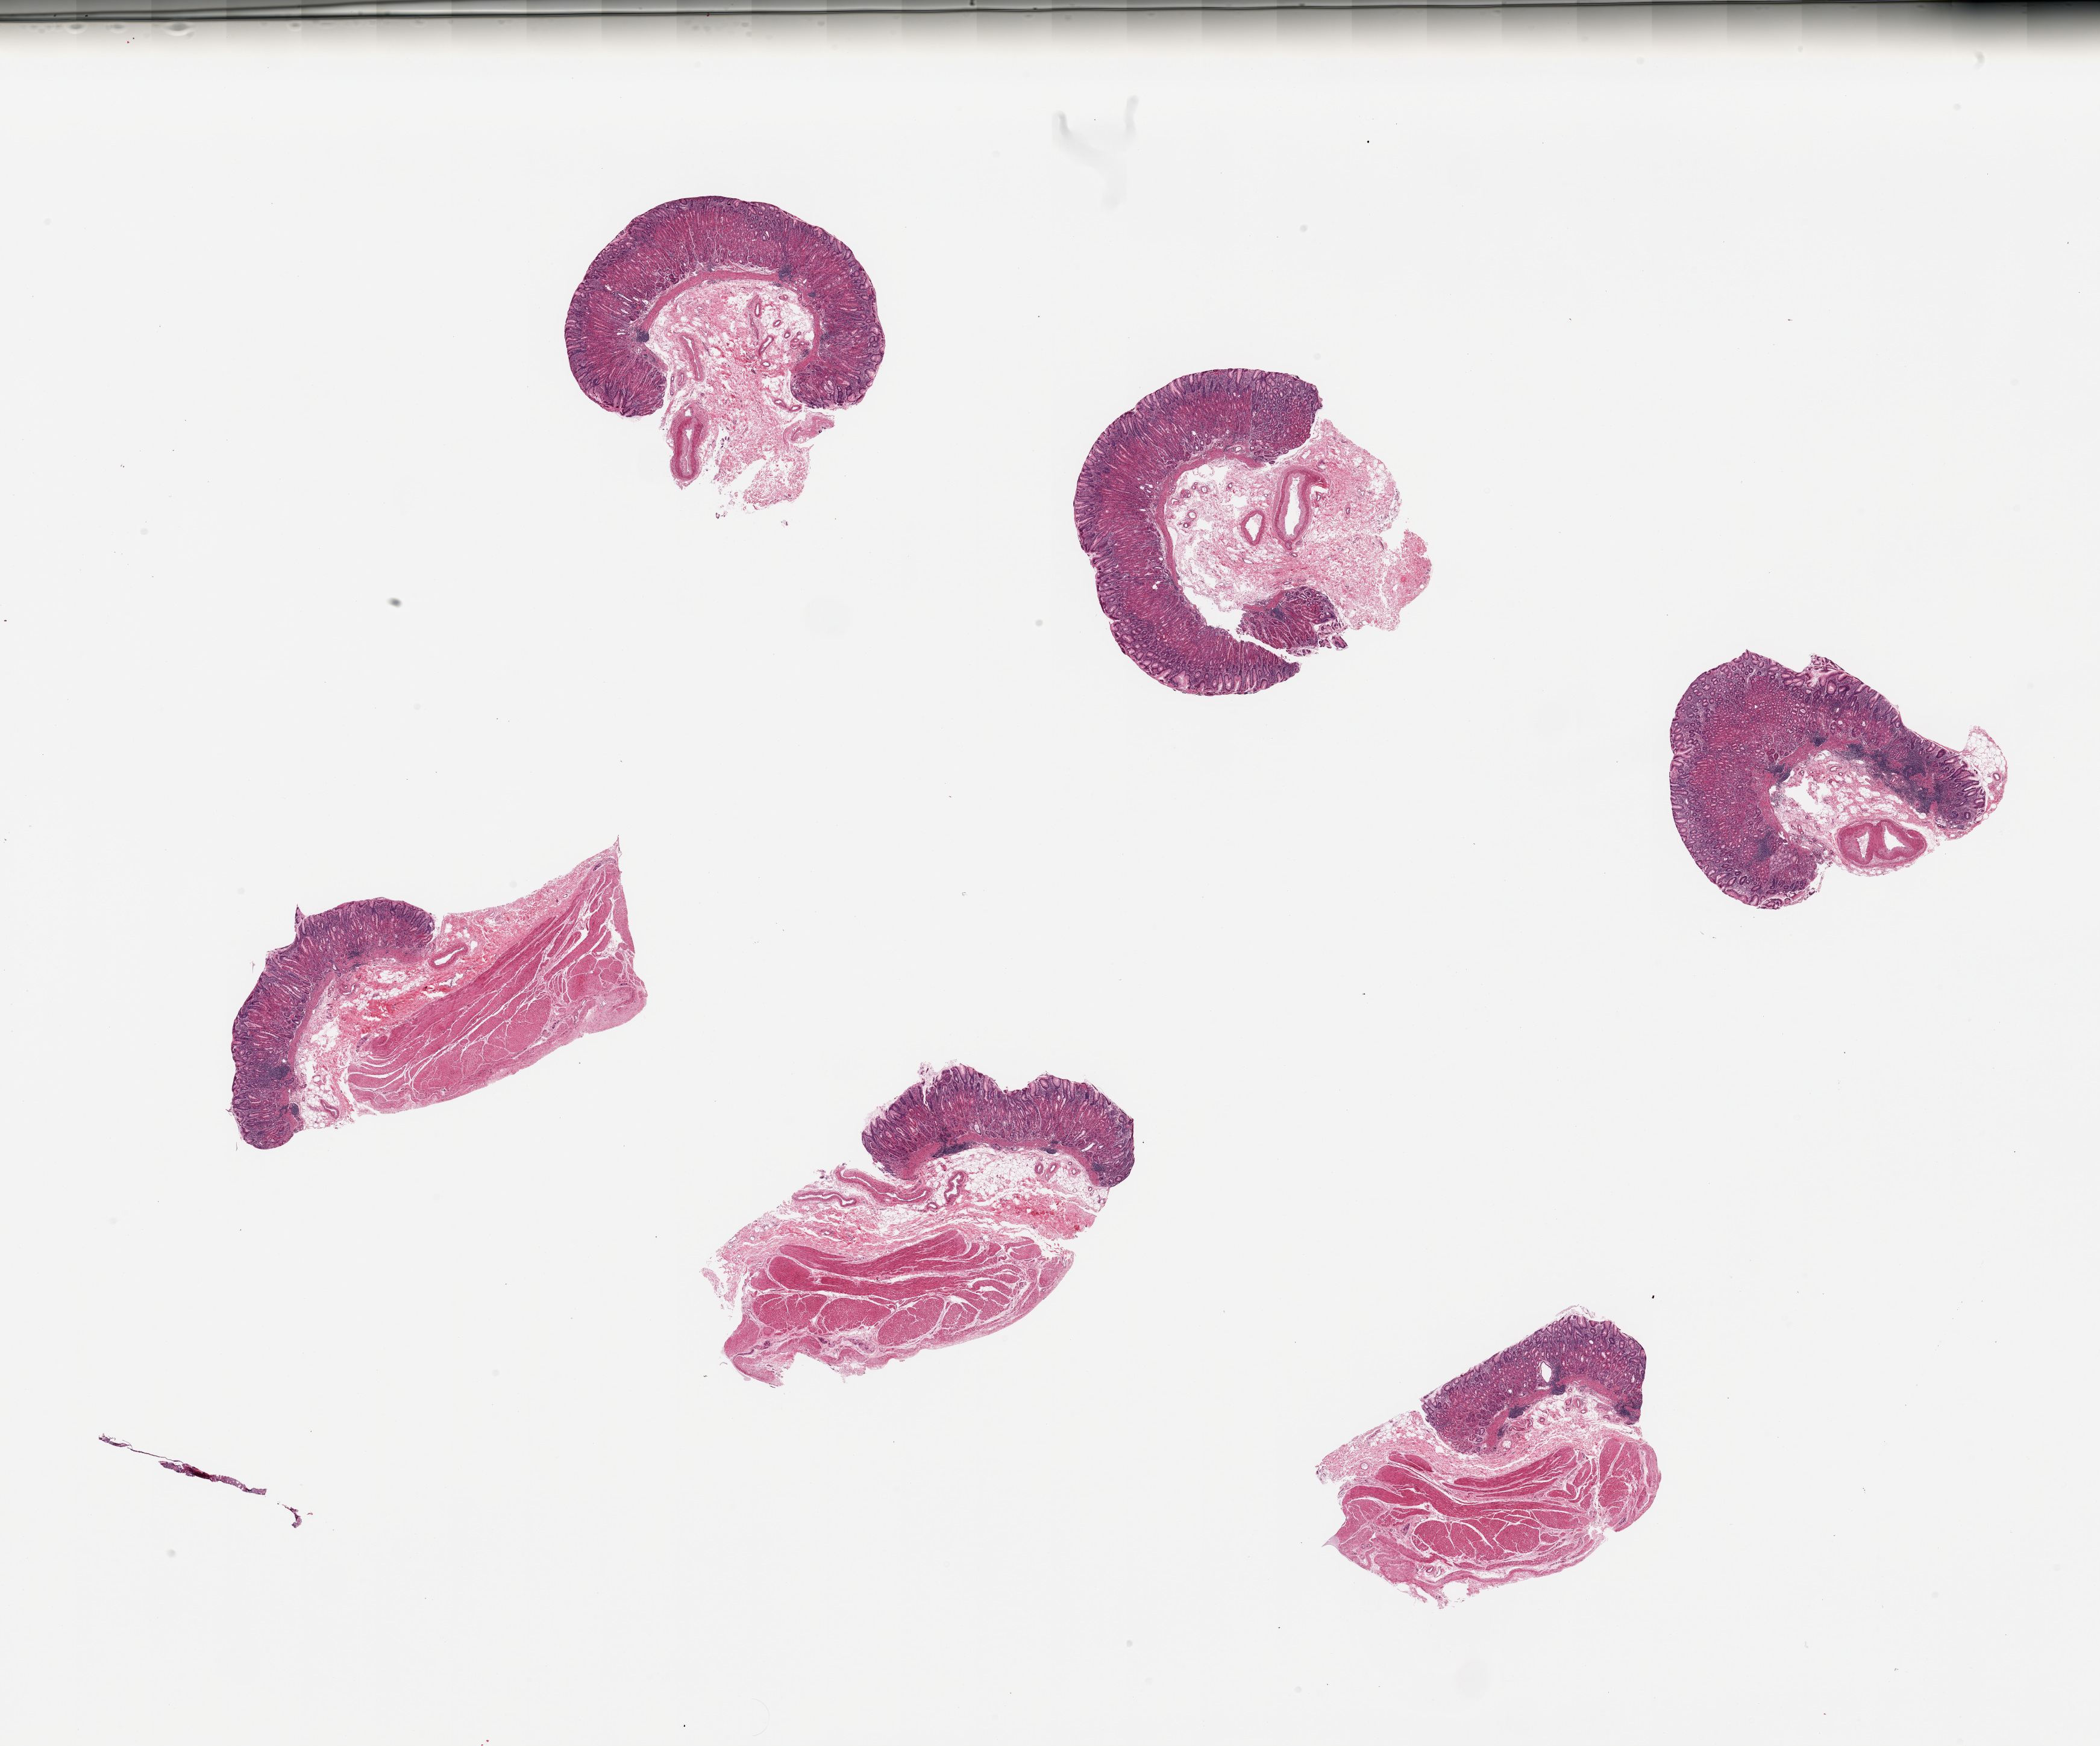
H&E whole-slide image, brightfield, a low-resolution overview of the entire scanned area, about 27.6 x 22.9 mm (acquisition: 20x scan); PAXgene-fixed paraffin-embedded (PFPE) section; section of stomach (target tissue); tissue donor sample. Donor: female.
Review note (as recorded): 6 pieces, well preserved mucosa ~1mm, 20-30% thickness.